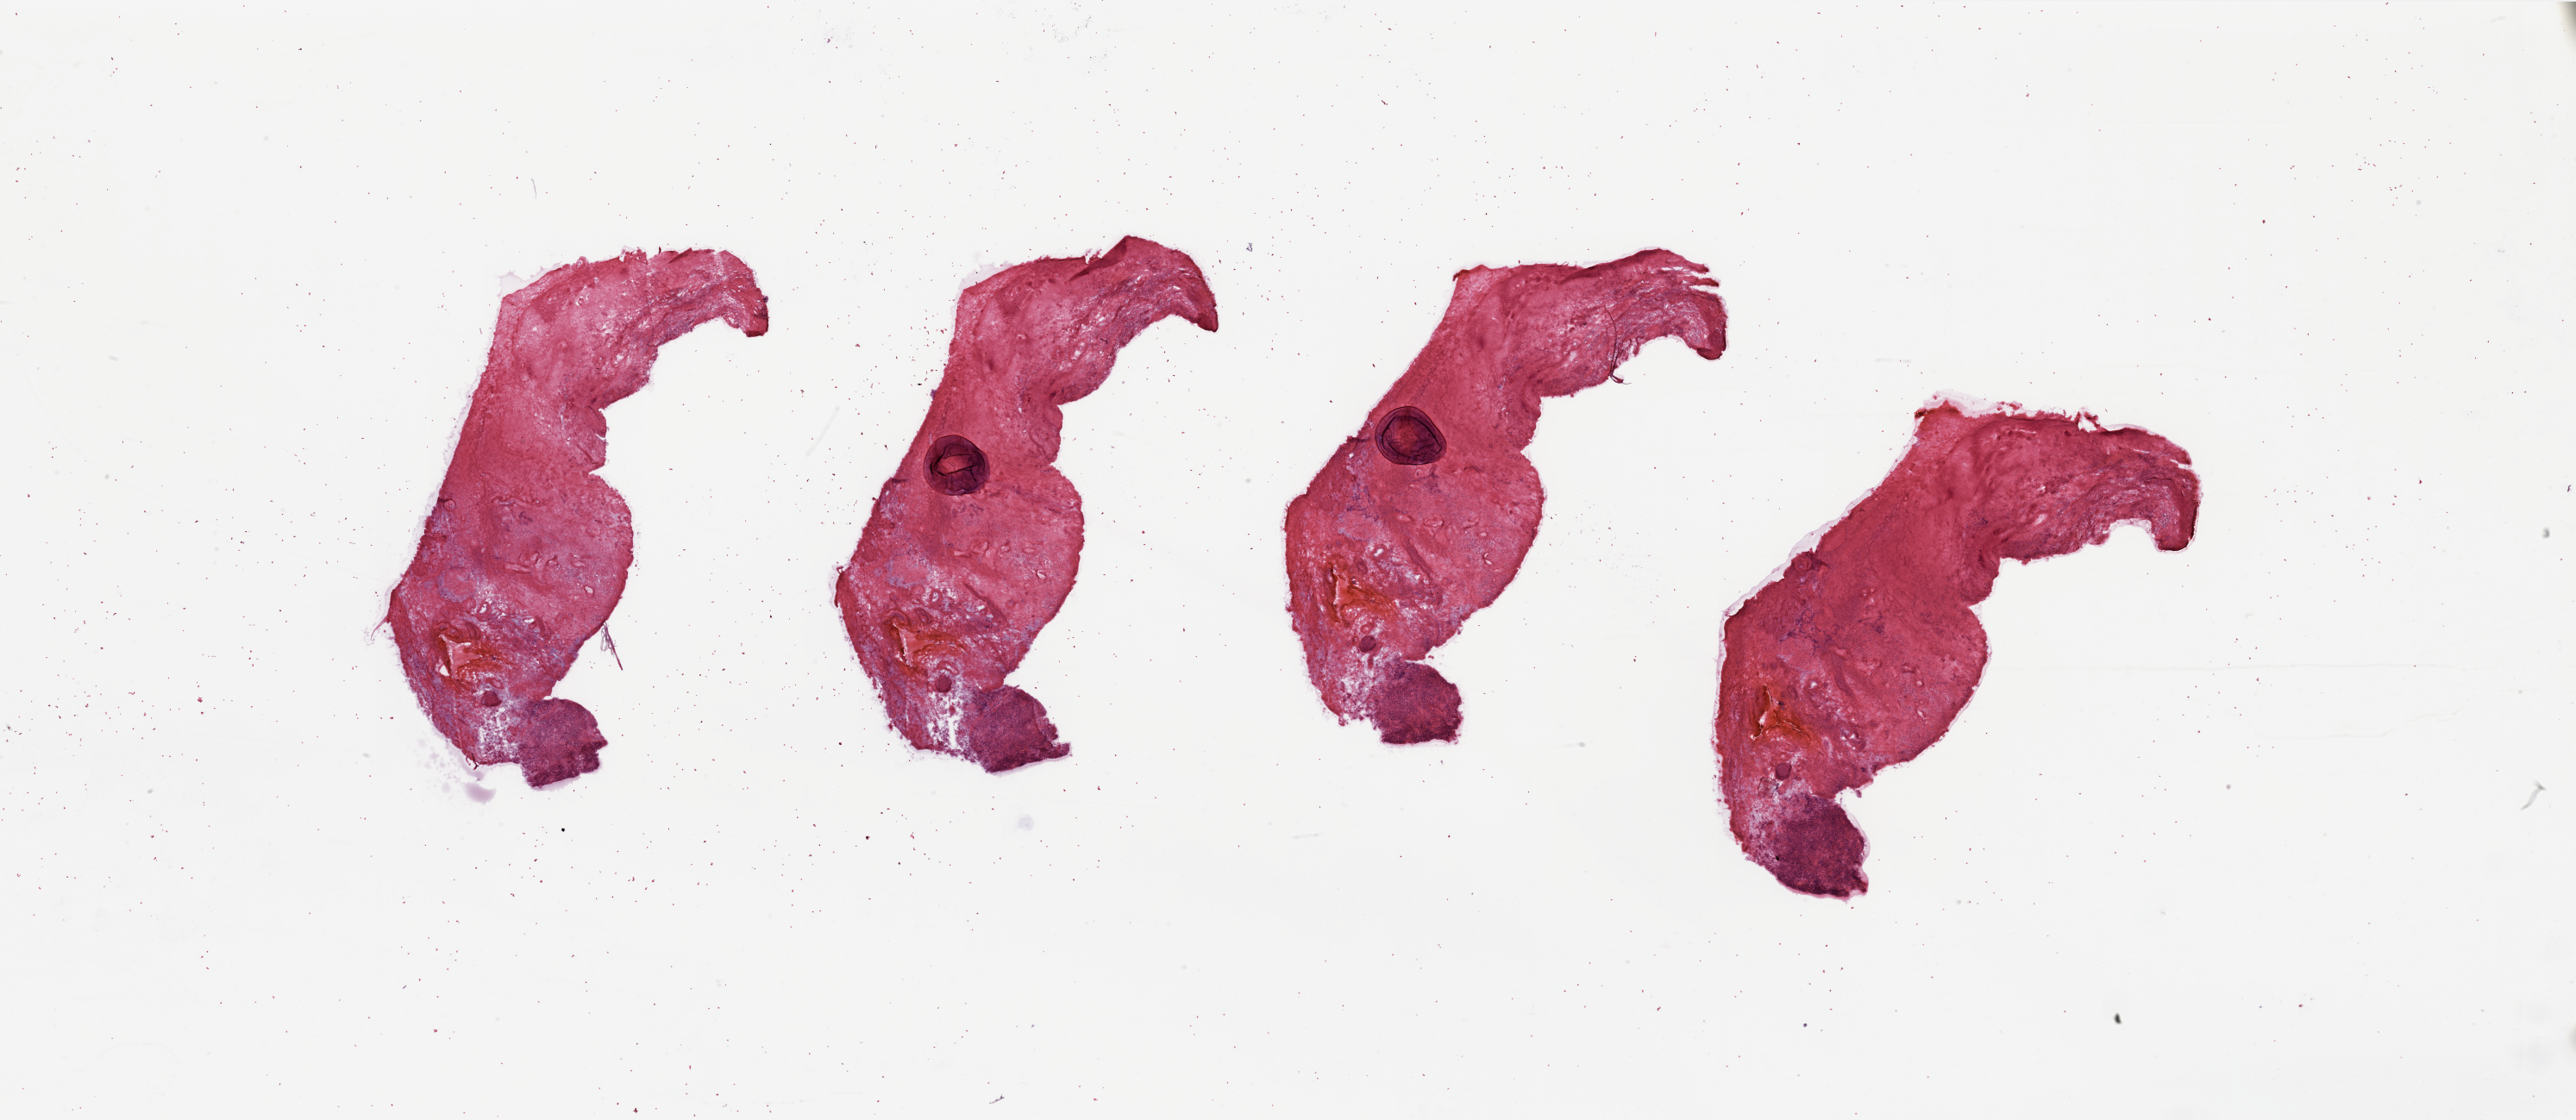
H&E-stained whole-slide image, shown as a low-resolution overview of the whole scanned area (about 47.3 x 20.5 mm, acquisition: 20x scan). Tumour tissue sample, sampled site: kidney. Male, 78 y/o. Histologic grade: G2 (moderately differentiated). Composition of this section per pathologist review: tumour nuclei 20%, necrosis 50%.
AJCC pathologic stage: I. Primary tumour site (as recorded): upper pole. Diagnosis: Renal cell carcinoma, NOS.